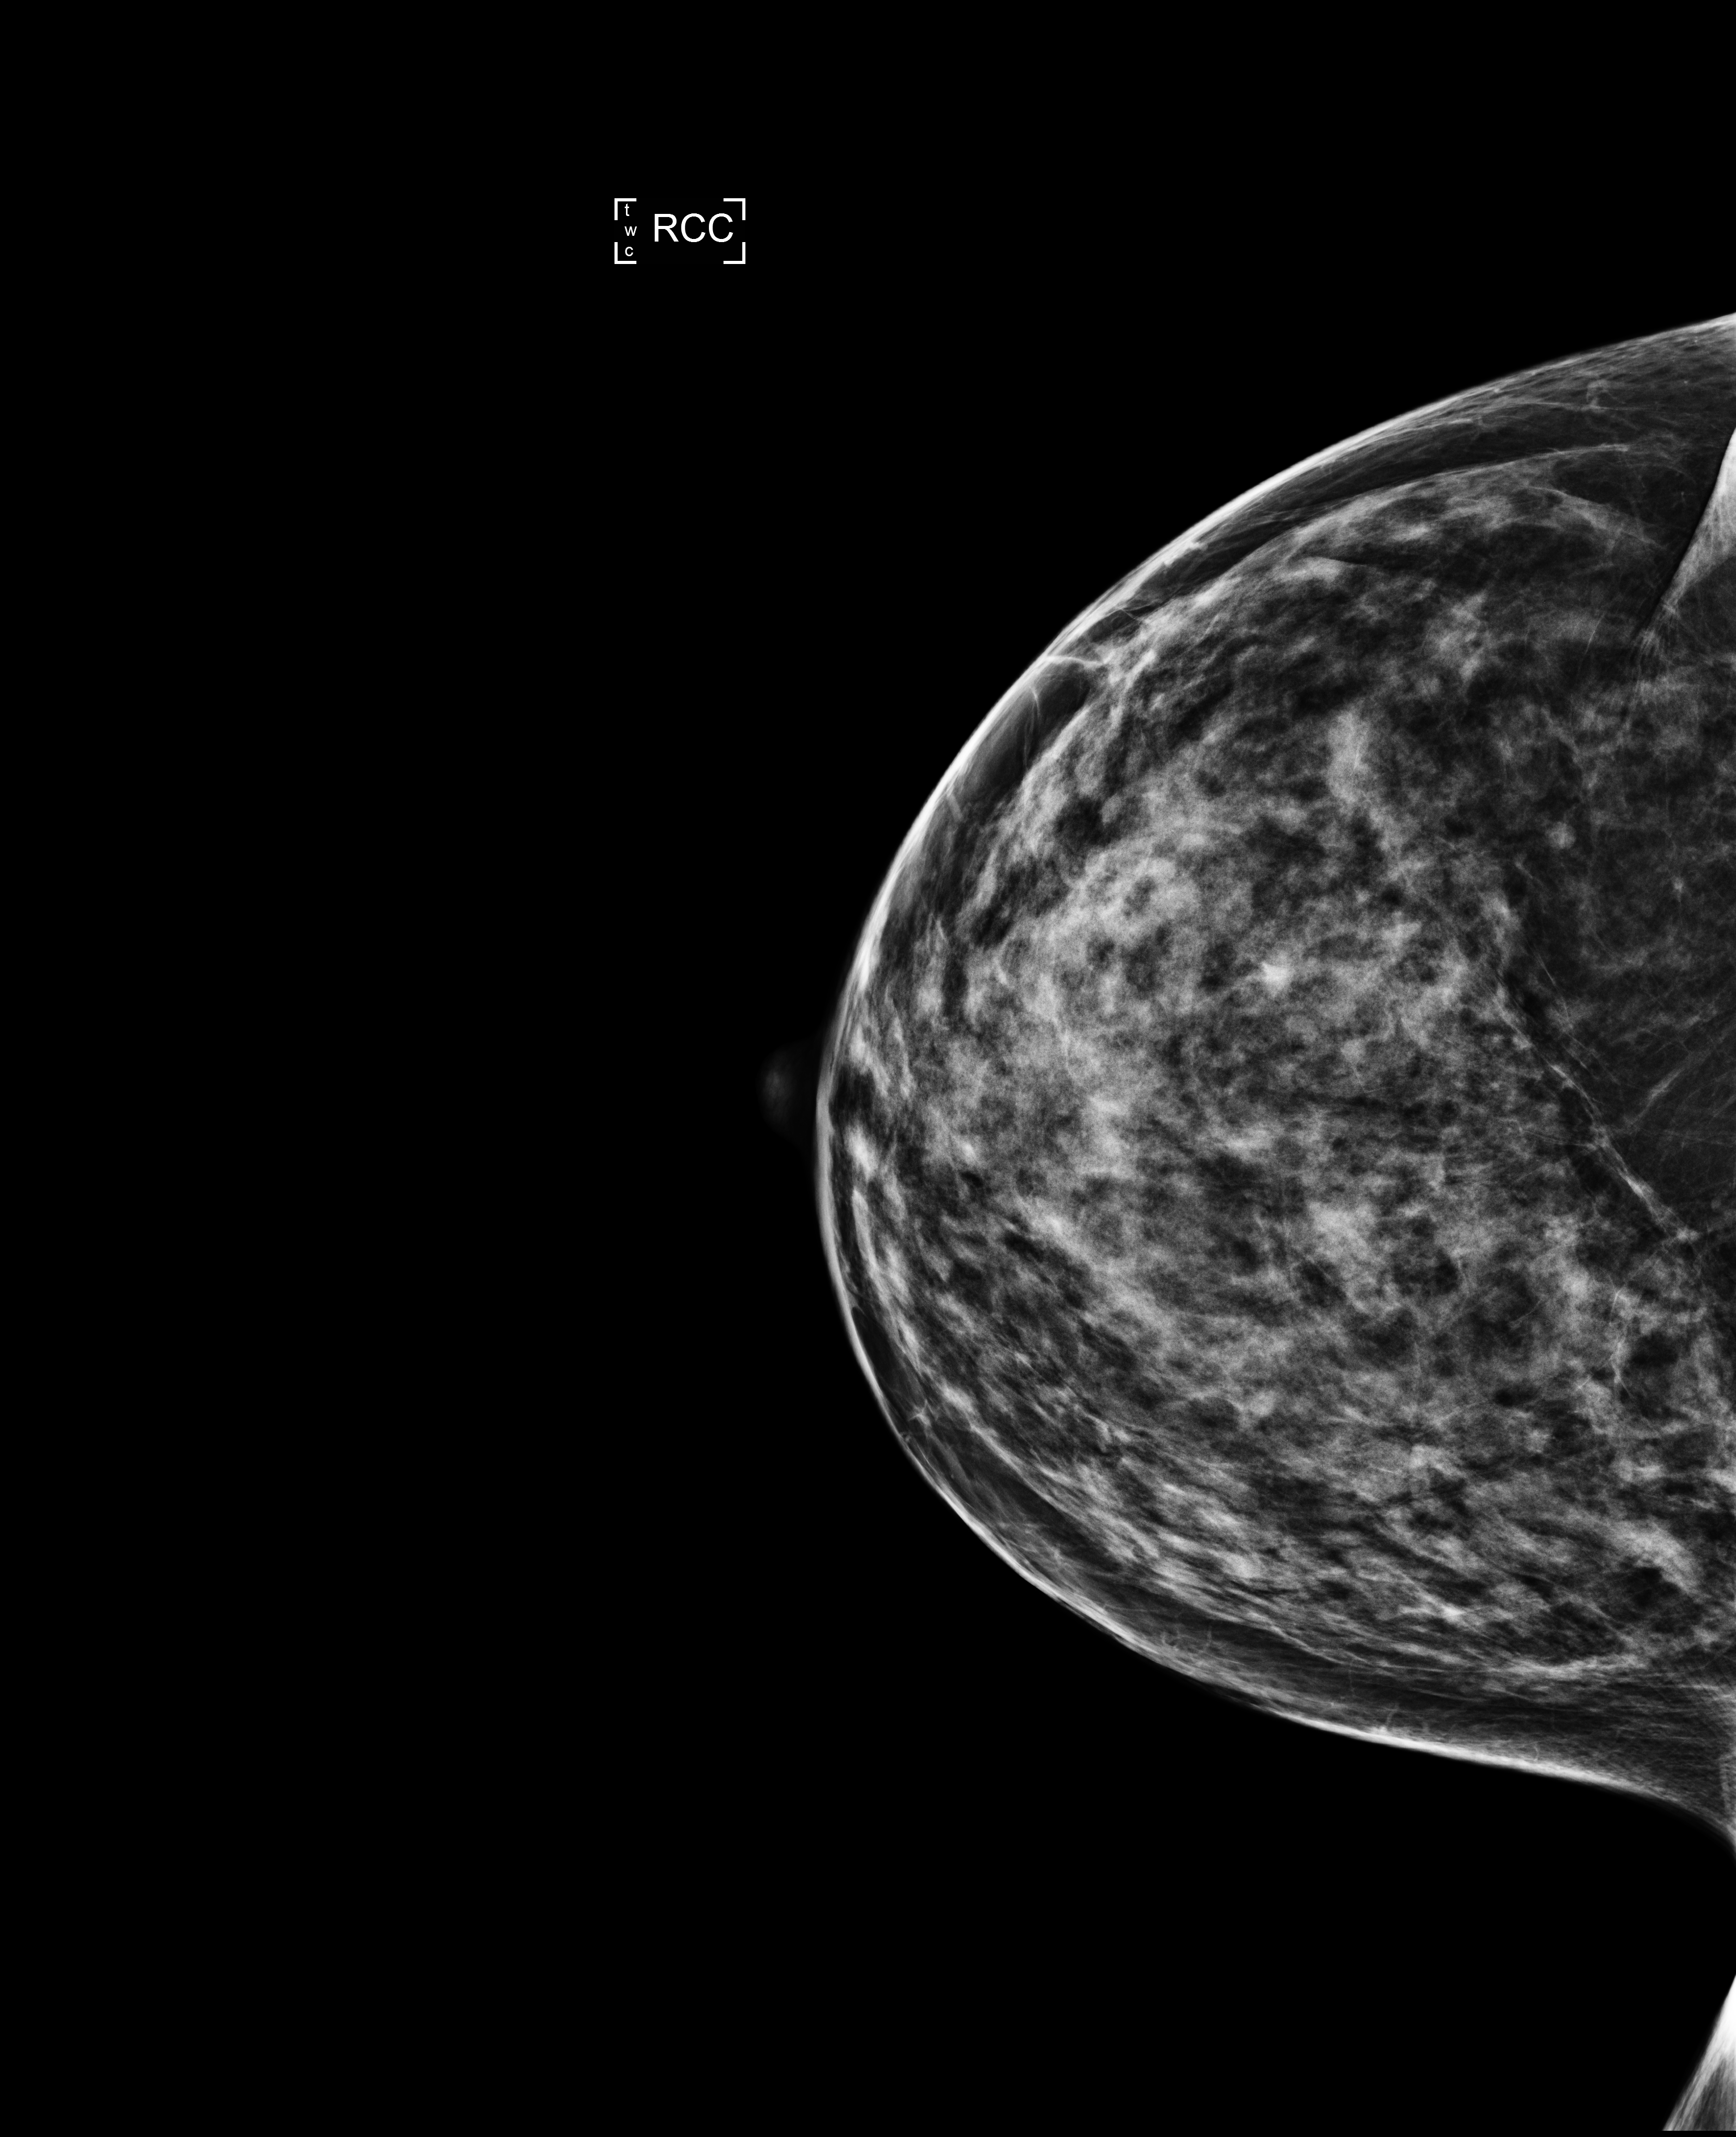
Digital mammogram (FFDM), right breast, CC view, annual screening mammography examination, system: Selenia Dimensions. Female patient, age 44 years.
Breast density at the screening exam (both breasts): heterogeneously dense (BI-RADS density category c). Final BI-RADS category for the screening round (tomosynthesis exam, both breasts): category 2. Recall: no recall after this screen.